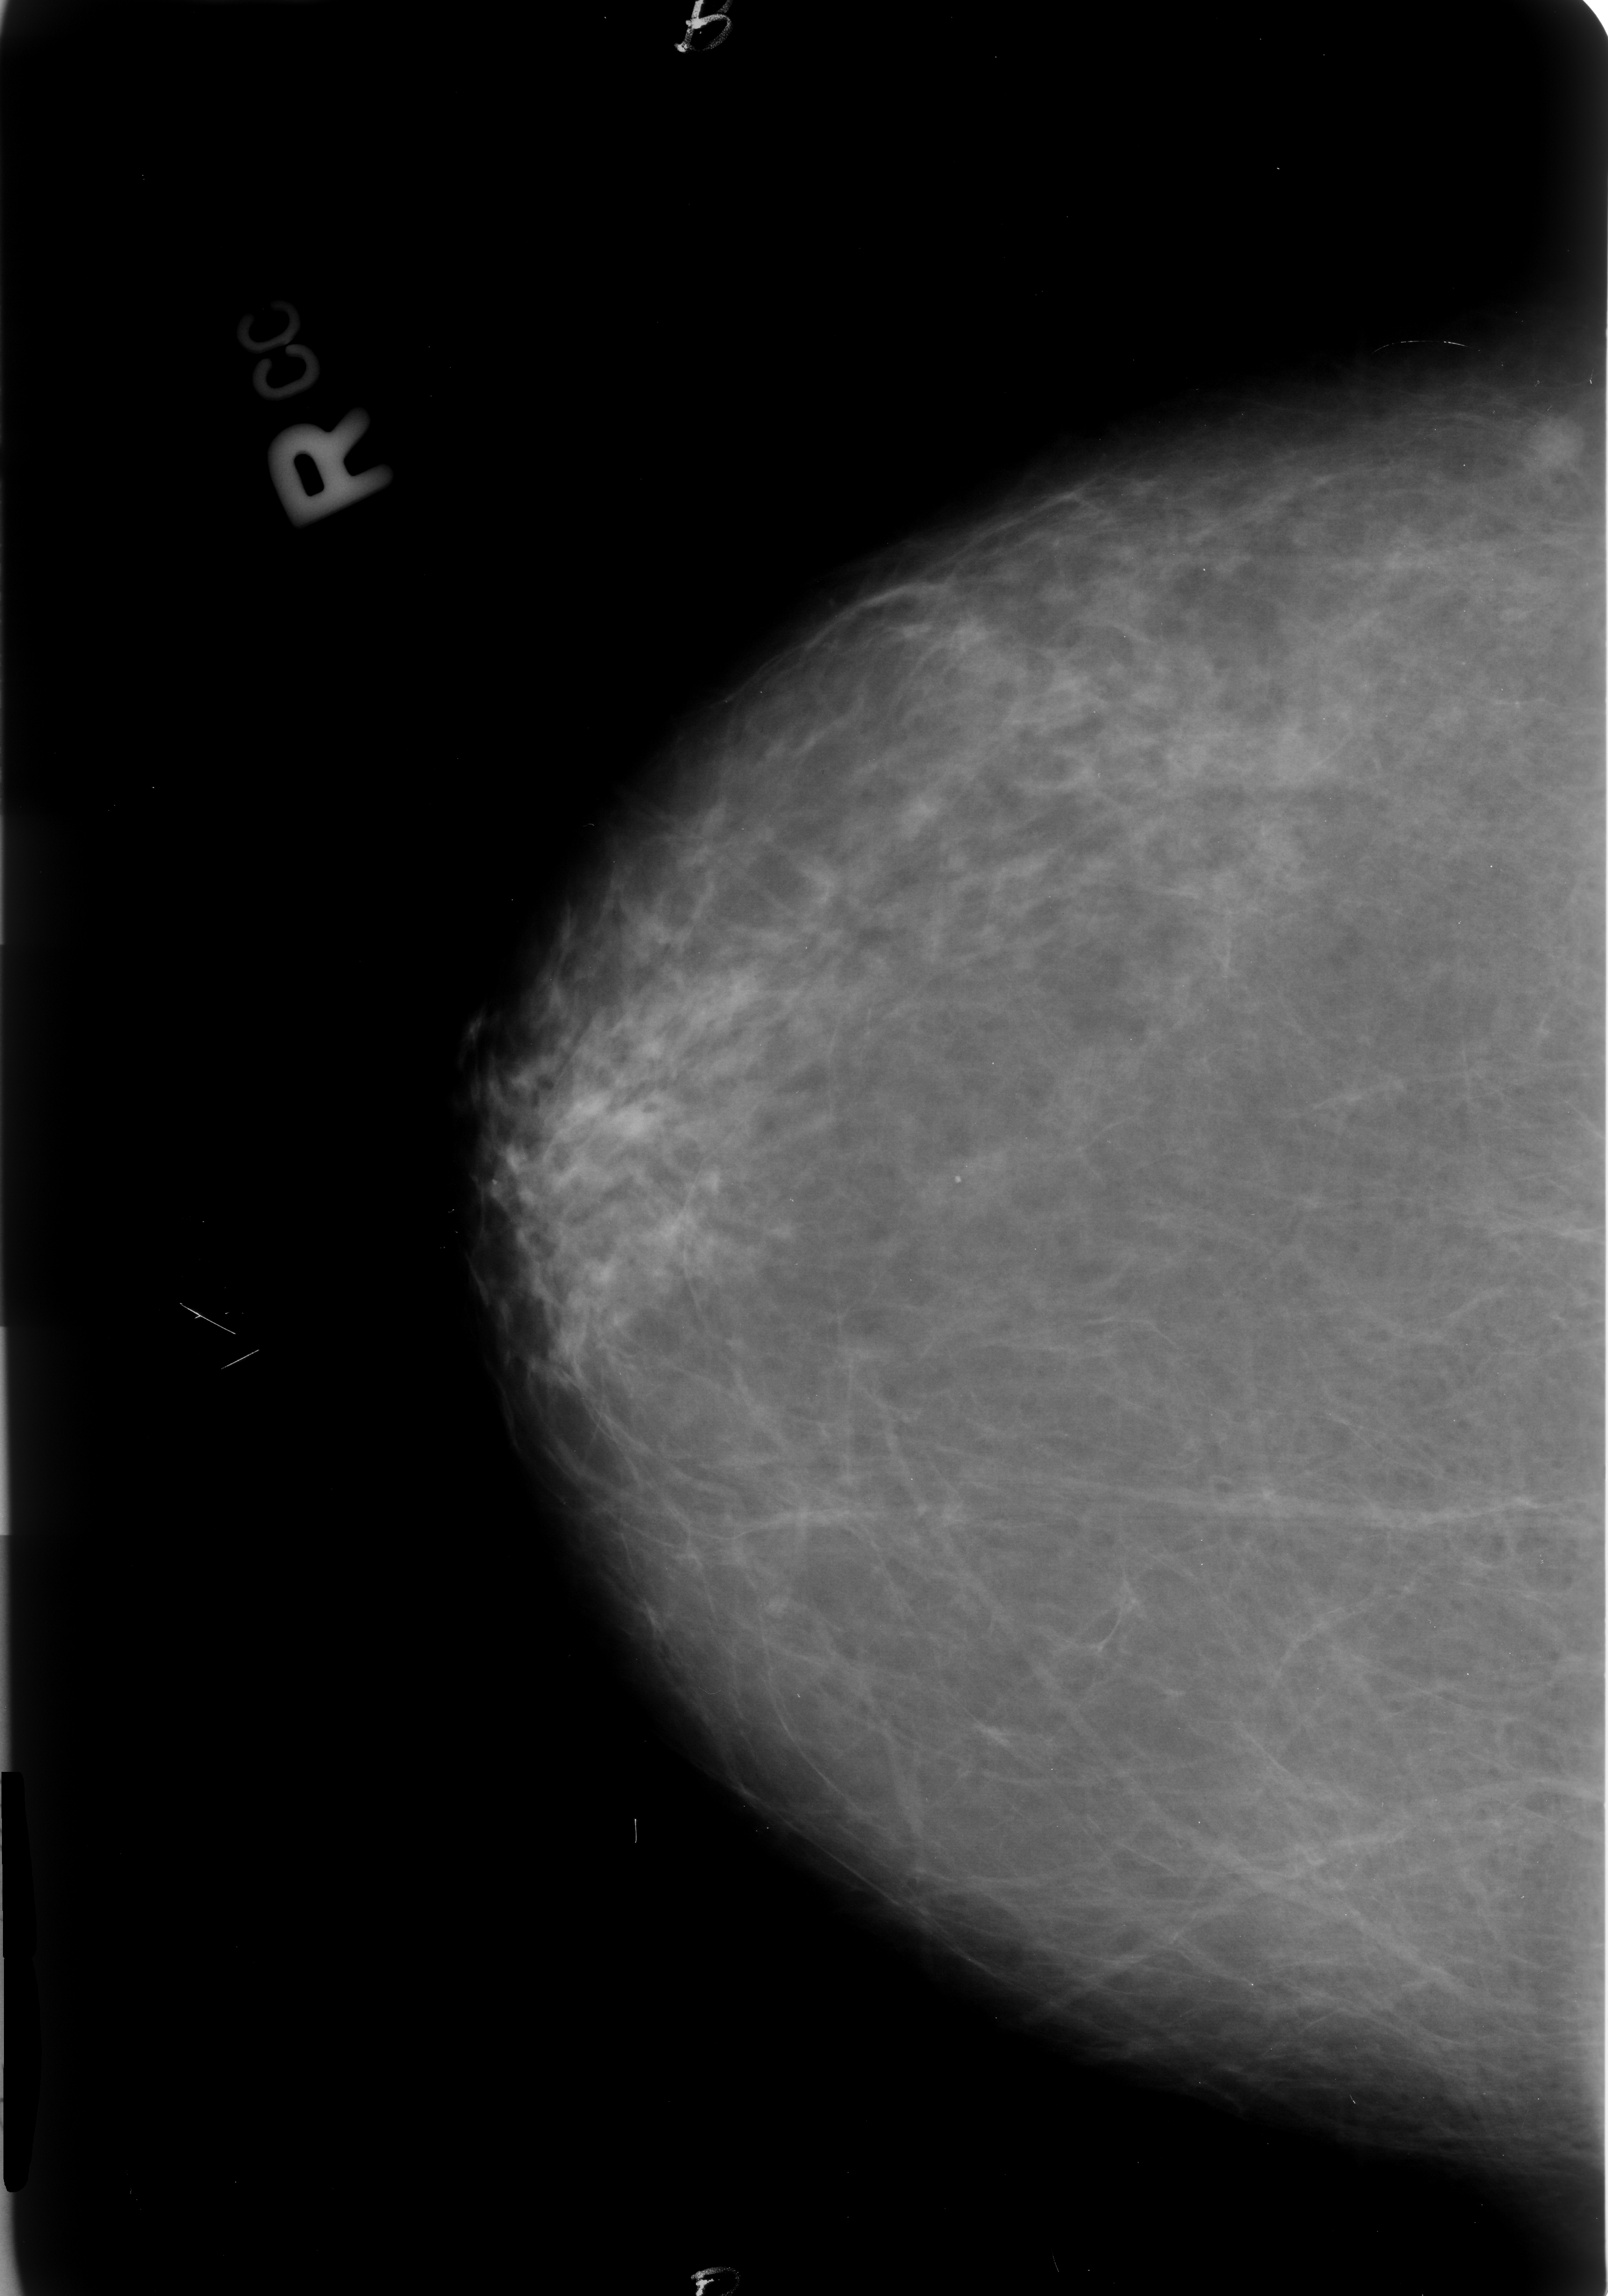
Digitized screen-film mammogram. Right breast. Craniocaudal (CC) view. 1608 × 2296 image matrix.
Marked abnormalities (boxes around the expert regions of interest):
- mass, shape oval, margins ill defined; BI-RADS assessment category 4; pathology (as recorded): malignant: bounding box [x1, y1, x2, y2] px = [1501, 395, 1588, 484]